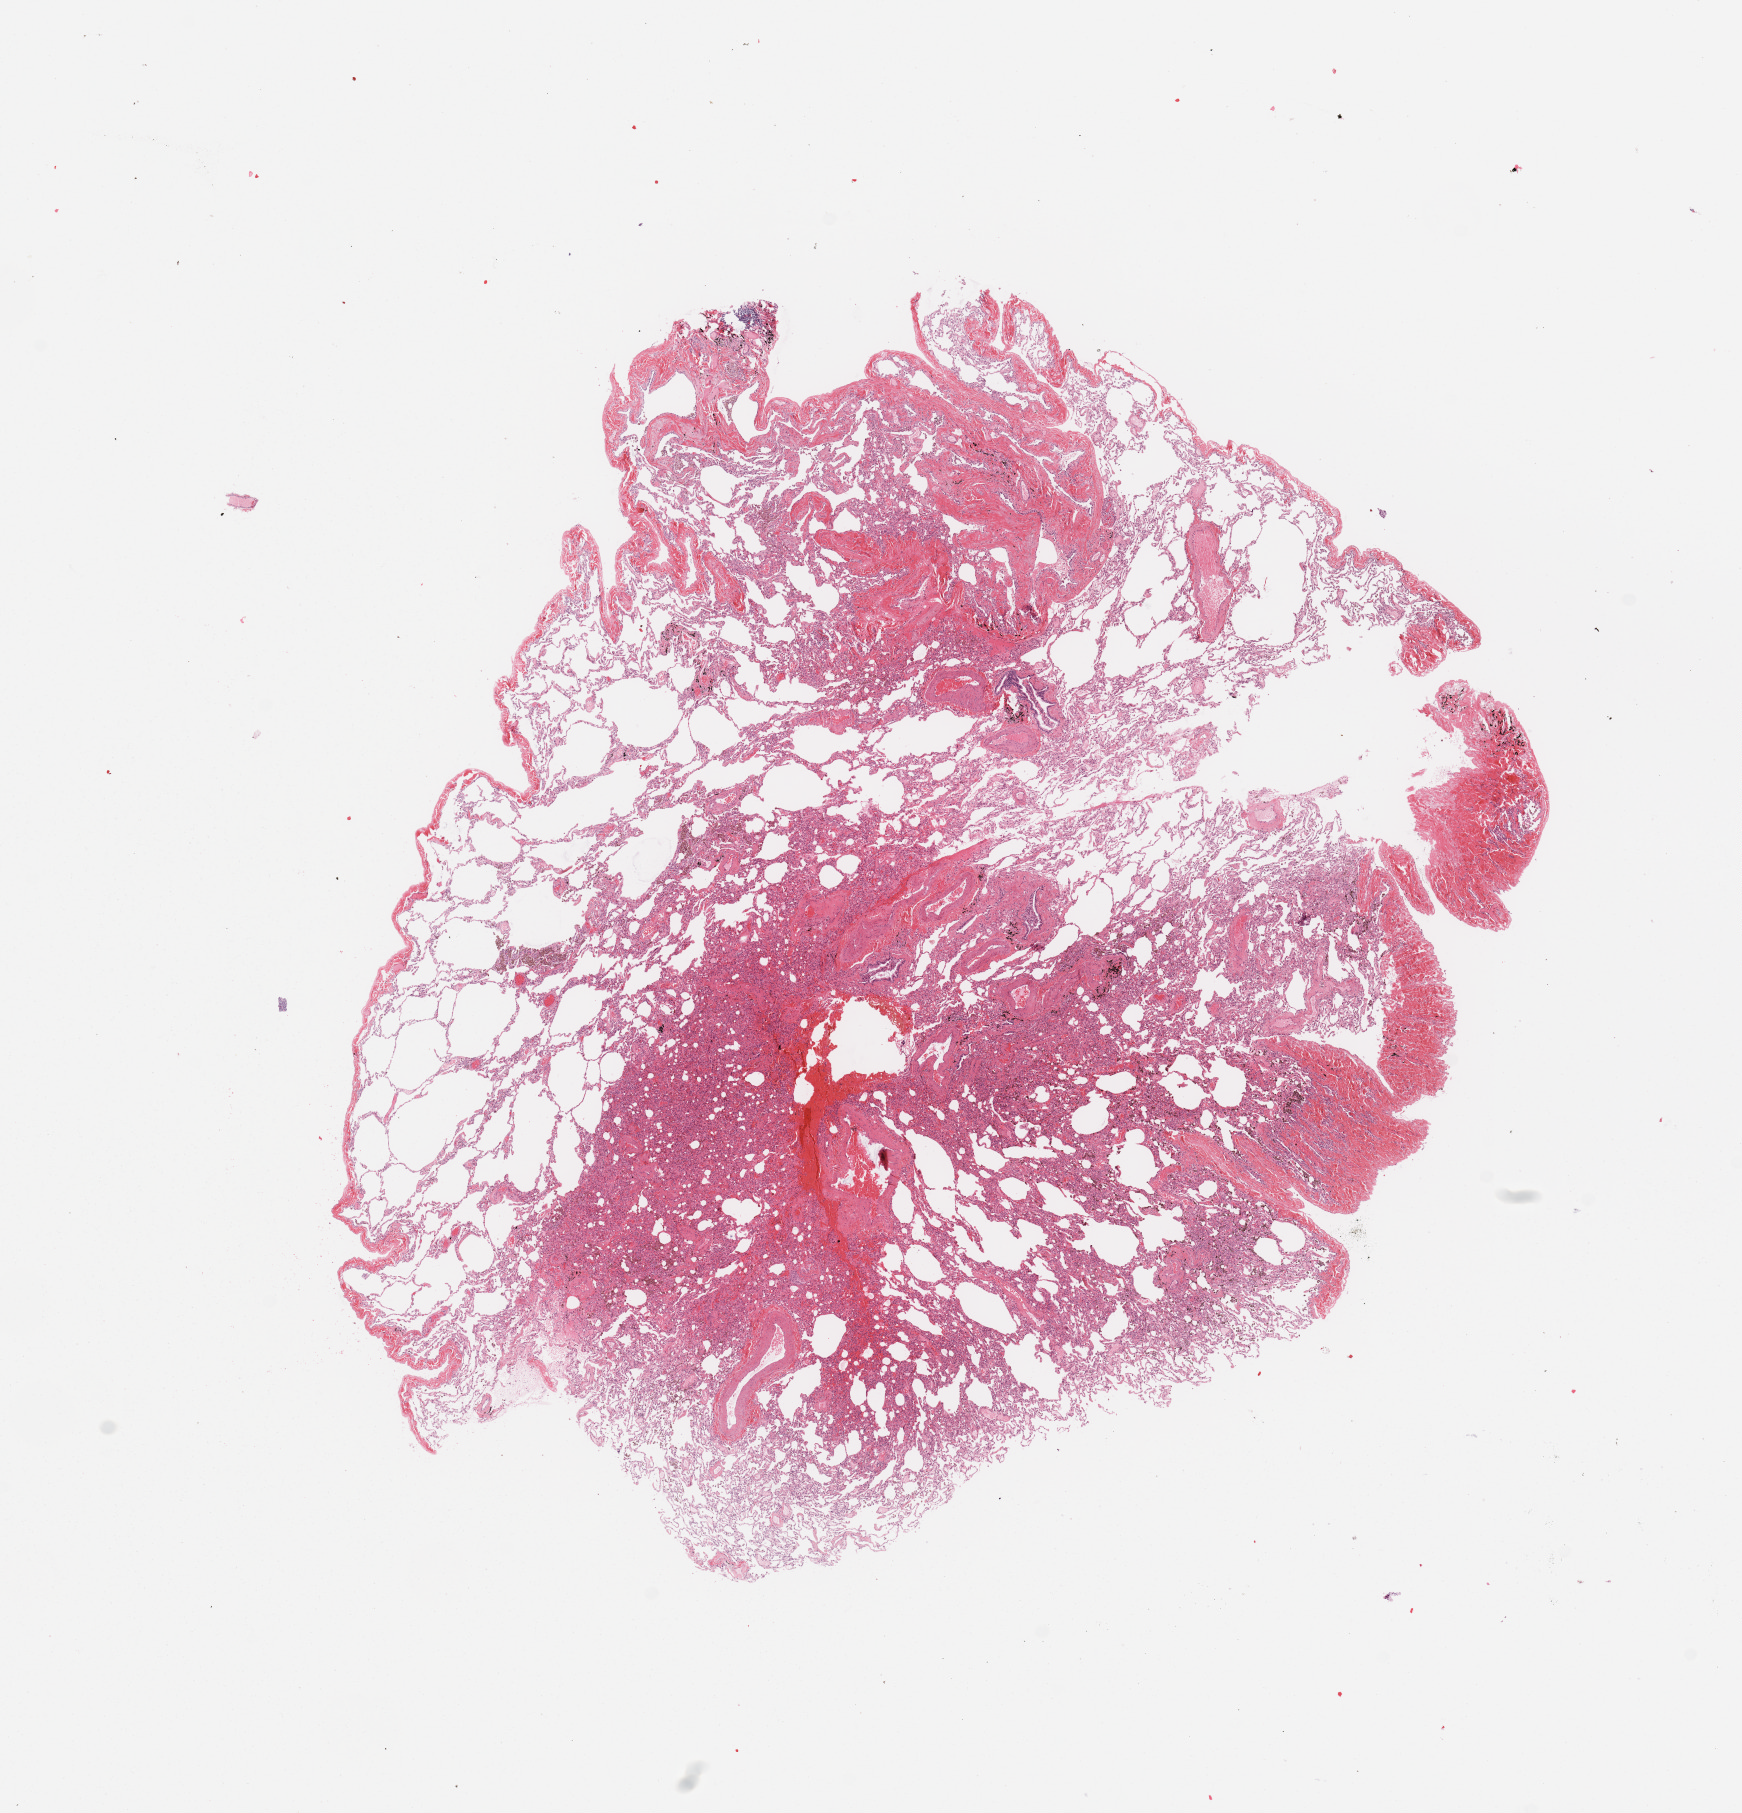
Digitized H&E tissue section (whole slide) — shown as a low-resolution overview of the whole scanned area (about 13.8 x 14.3 mm), normal (non-tumour) tissue sample, sampled site: lung. Male, 62 y/o.
This section: normal (non-tumour) tissue from the same patient. Patient diagnosis: Adenocarcinoma, NOS.